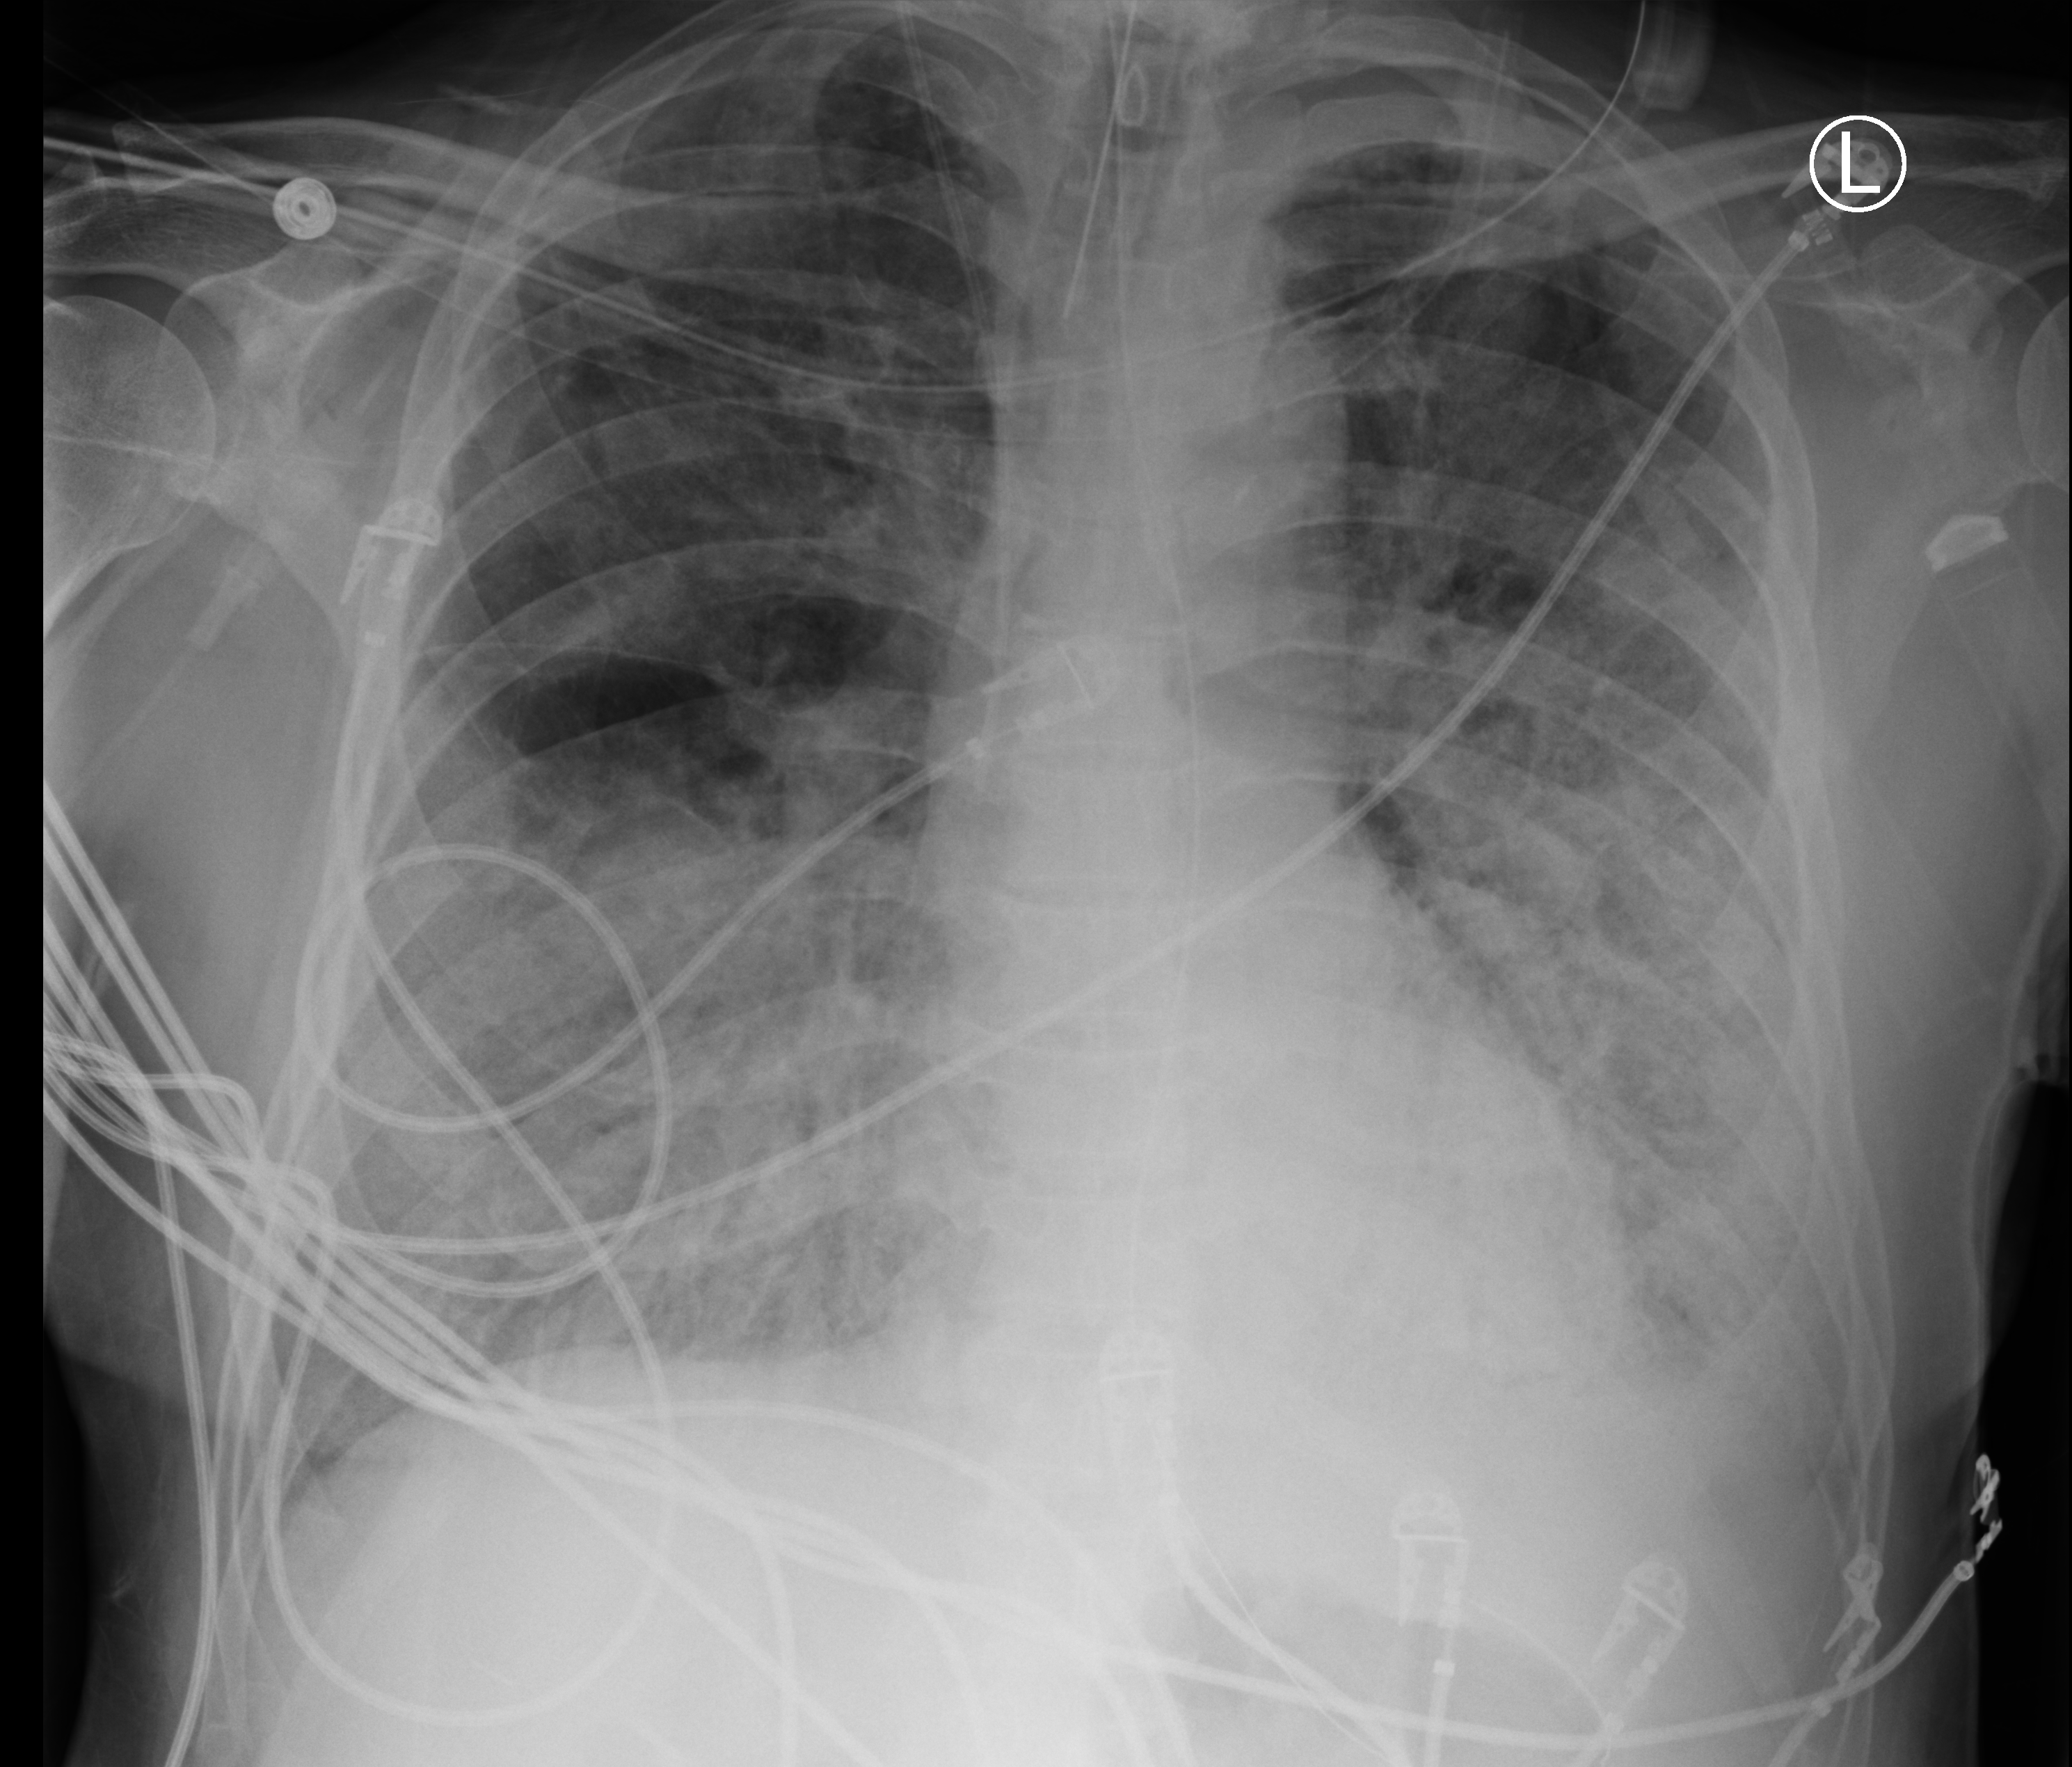
Portable chest radiograph, anteroposterior (AP) projection. Patient hospitalised with COVID-19; male, aged 60–74 years.
Hospital-stay facts (about this admission, not read from this image; timing relative to this image not recorded): admitted to intensive care during this hospital stay: yes.